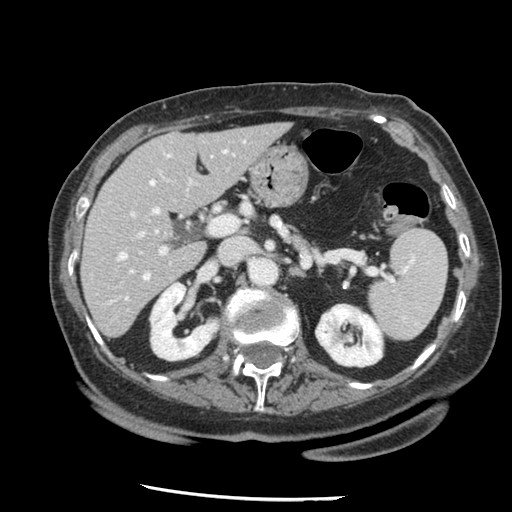
Contrast-enhanced abdominal CT, one axial slice; position 75 of 148 along the scan axis; intravenous contrast given; soft-tissue window (W 400 / L 40 HU); 2.5 mm slice thickness; 512 × 512 image matrix, field of view 330 × 330 mm. Female patient, age 85 years. Case-level facts recorded for this patient, not image findings: diagnosis: colorectal cancer liver metastases, imaged before liver resection.
Outlined on this slice (expert manual segmentation):
- hepatic veins: bounding box [x1, y1, x2, y2] px = [119, 142, 176, 300]
- liver: [83, 124, 288, 337]
- planned liver remnant (the part of the liver to remain after resection): [83, 124, 288, 337]
- portal vein (with intrahepatic branches): [129, 148, 230, 274]